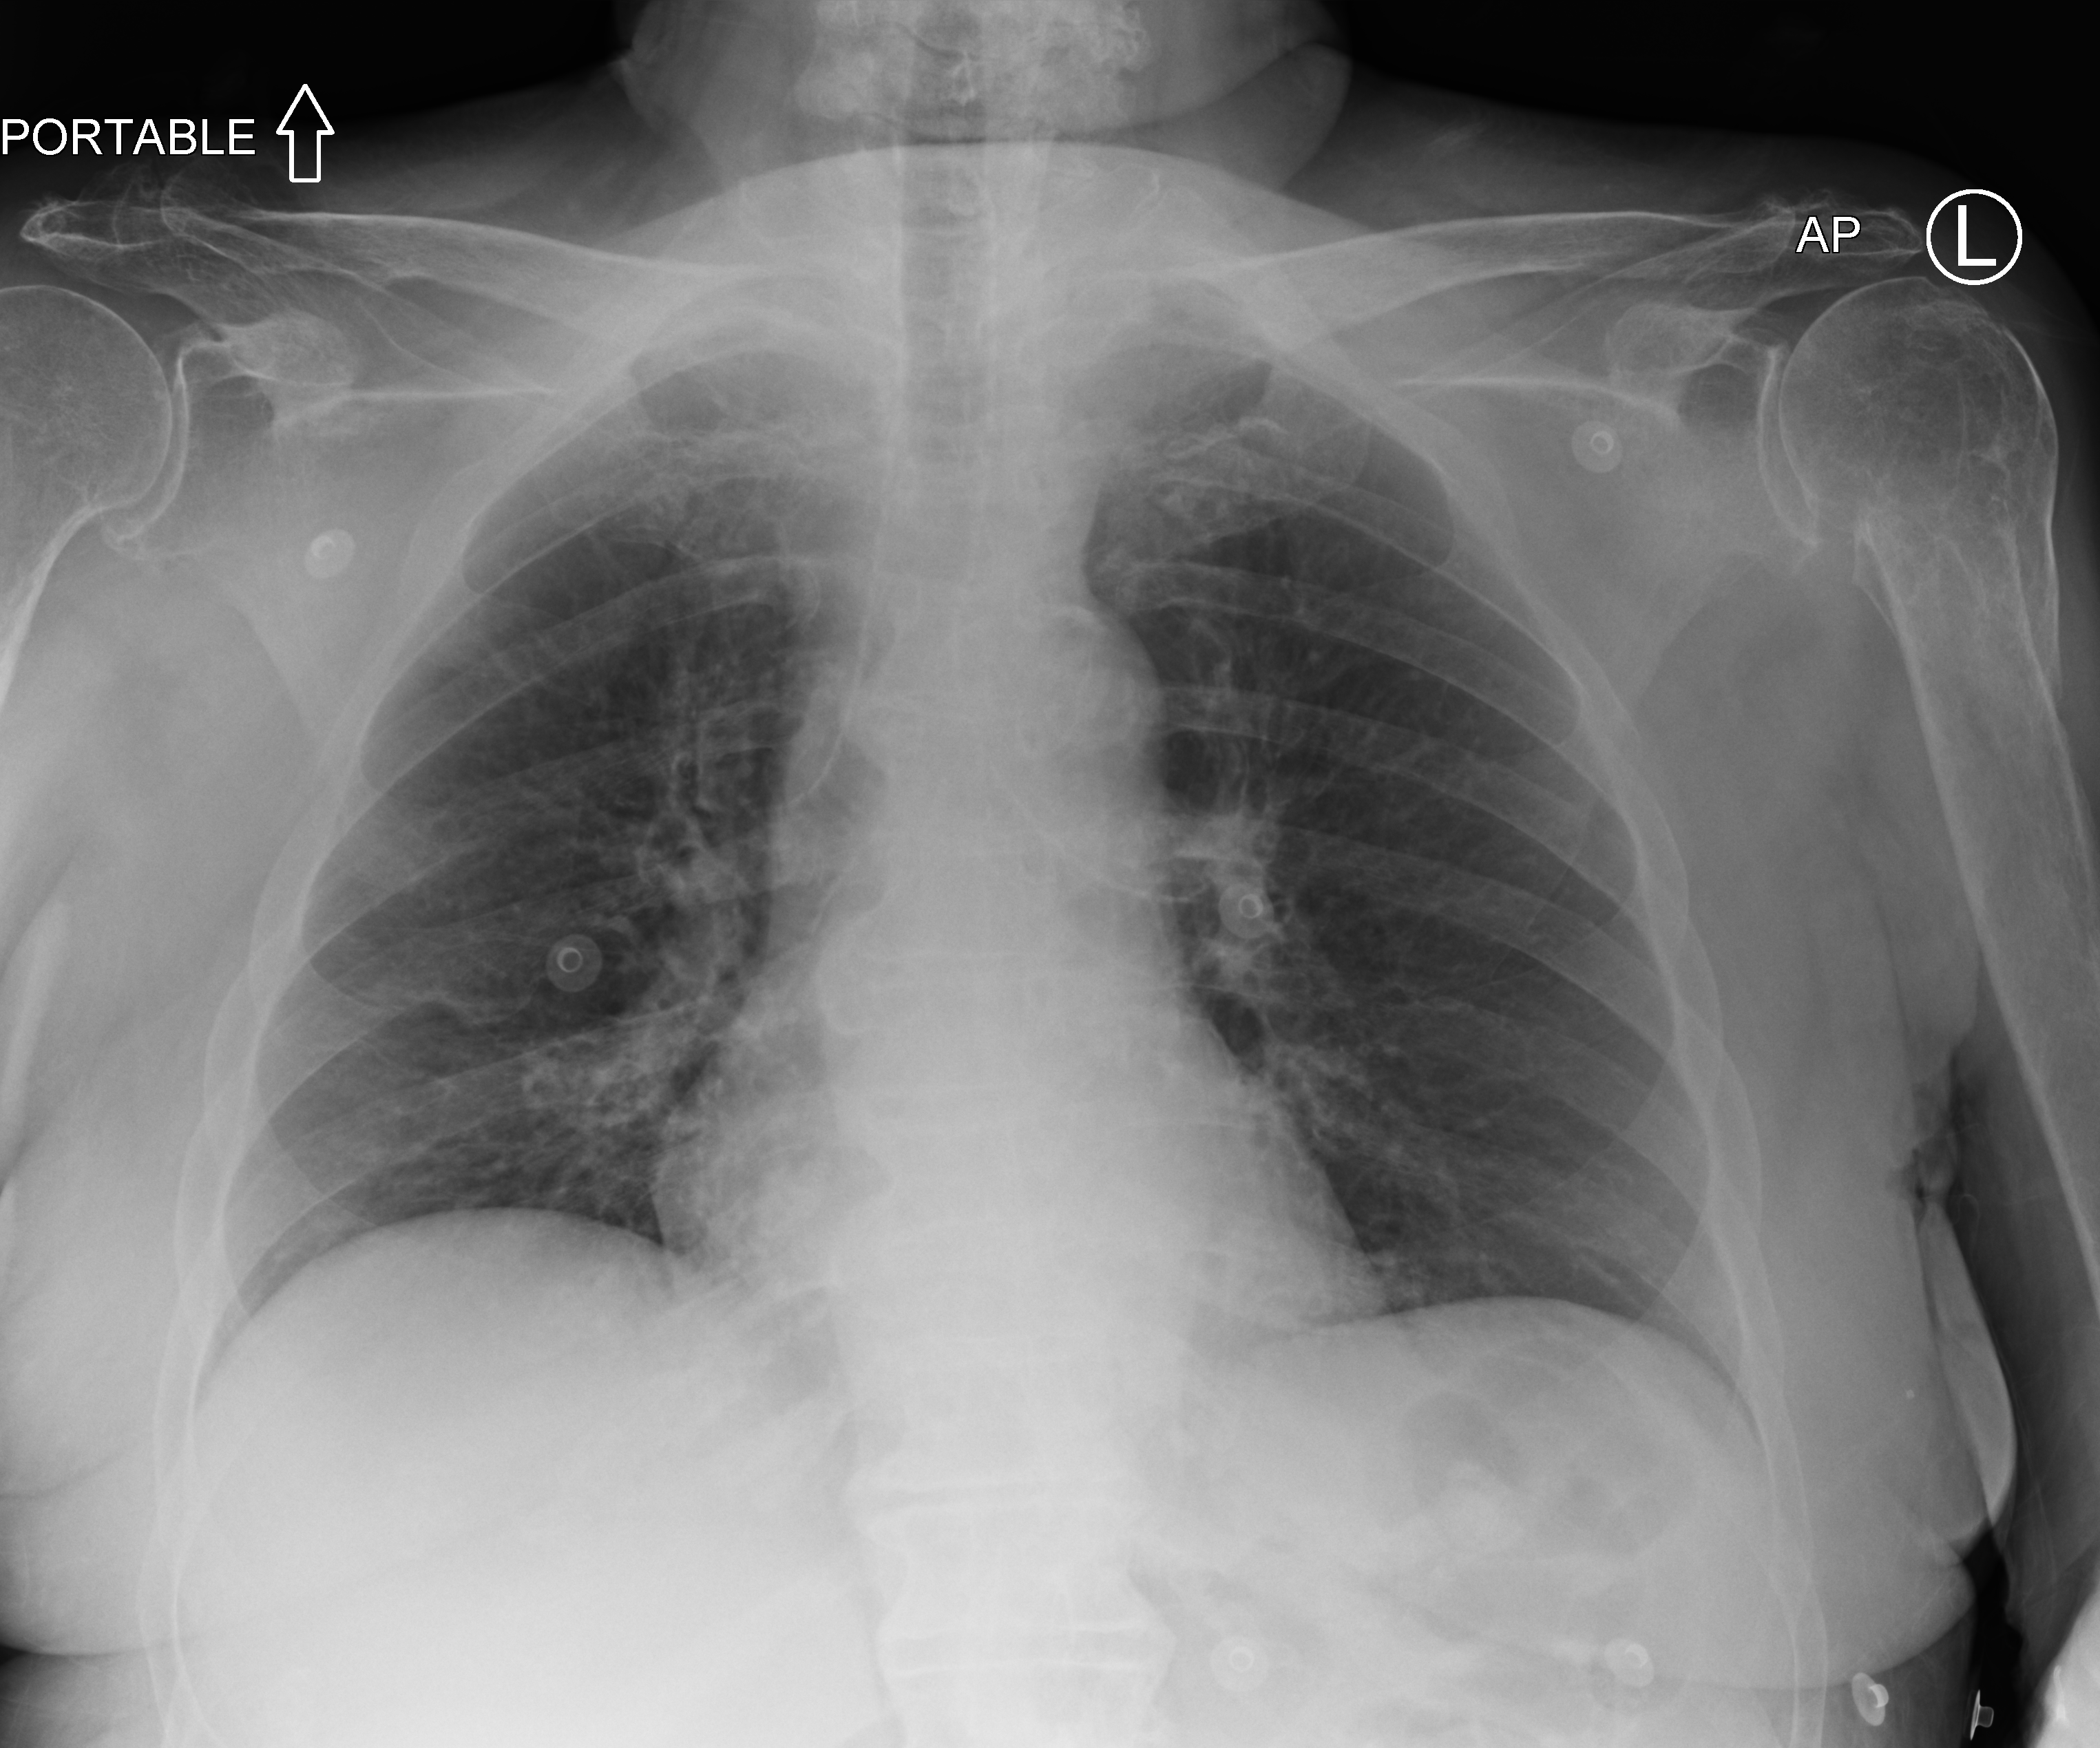
Portable chest radiograph, anteroposterior (AP) projection. Female patient hospitalised with COVID-19, age 75–90 years.
Hospital-stay facts (about this admission, not read from this image; timing relative to this image not recorded): admitted to intensive care during this hospital stay: no.